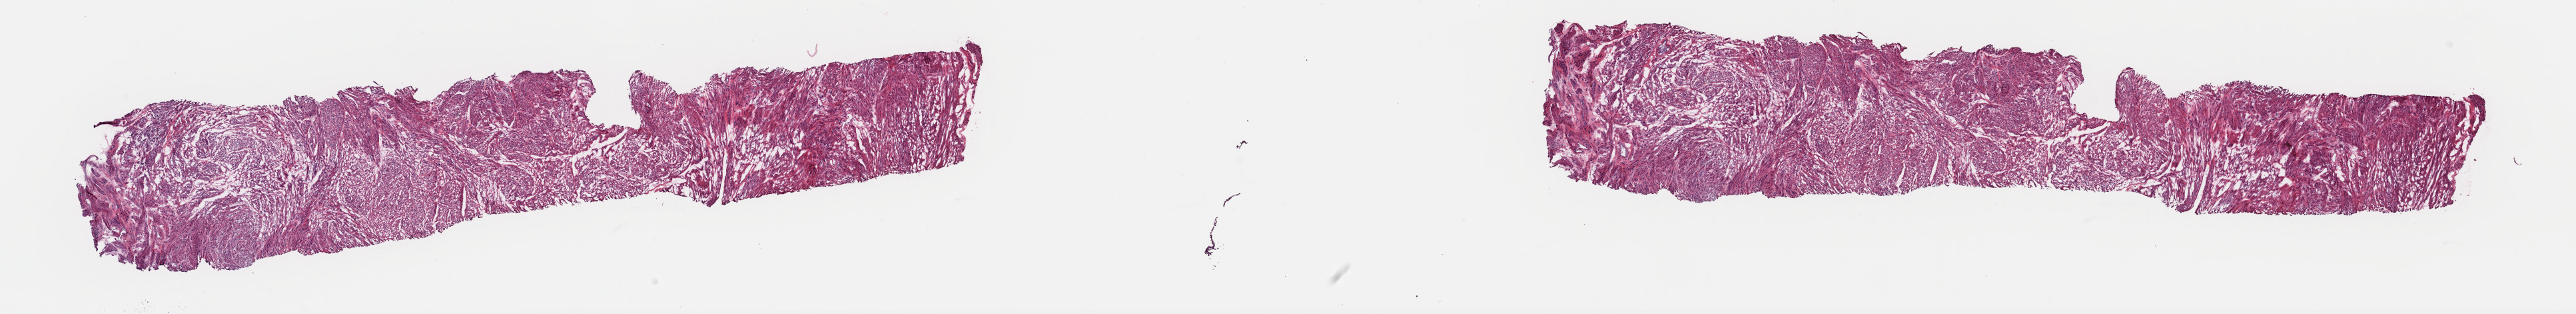
Digitized H&E tissue section (whole slide) — shown as a low-resolution overview of the whole scanned area (about 30.5 x 3.7 mm, from a 40x scan), frozen section, retroperitoneum and peritoneum, primary tumour sample. Male, age 44 years at initial diagnosis. Slide review estimates, as recorded: tumour cells 100%, tumour nuclei 98%, normal cells 0%, stromal cells 0%, necrosis 0%. Infiltration values recorded for this section: lymphocyte infiltration 0%, monocyte infiltration 0%, neutrophil infiltration 0%.
Pathologic diagnosis: Leiomyosarcoma, NOS (retroperitoneum).